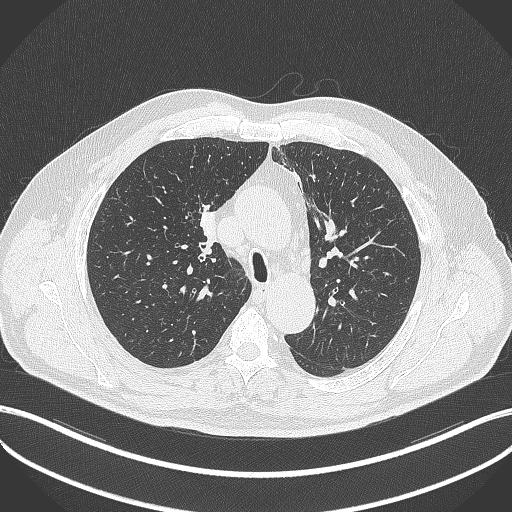
Chest CT, one axial slice. Position 266 of 411 along the scan axis. 120 kVp. Lung window (W 1500 / L -600 HU). 1 mm slice thickness. 512 × 512 image matrix, field of view 400 × 400 mm. Patient: male, 60 years. From the clinical record (not read from this slice): clinical TNM (as recorded): T1b N1 M0.
Annotated regions visible in this slice (bounding box drawn by a radiologist):
- lung tumour (recorded histology: squamous cell carcinoma): bounding box <190,204,223,253> (left, top, right, bottom; pixels)